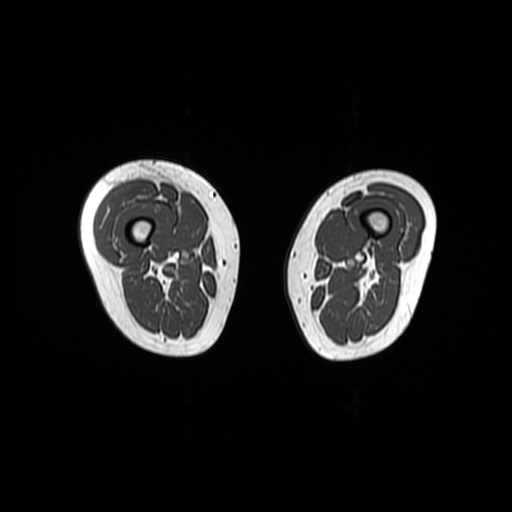
MRI of an extremity soft-tissue mass, one axial slice. Slice 12 of 48 in the series (ordered by position). 6 mm slice thickness. 512 × 512 image matrix, field of view 440 × 440 mm. Female patient. From the clinical record (not read from this slice): histological type: pleiomorphic undifferentiated sarcoma; grade: high; site of the primary tumour: right quadricep.
Structures marked on this image (manually delineated by an expert):
- gross tumour volume including surrounding oedema: box from (x=95, y=182) to (x=155, y=240) px